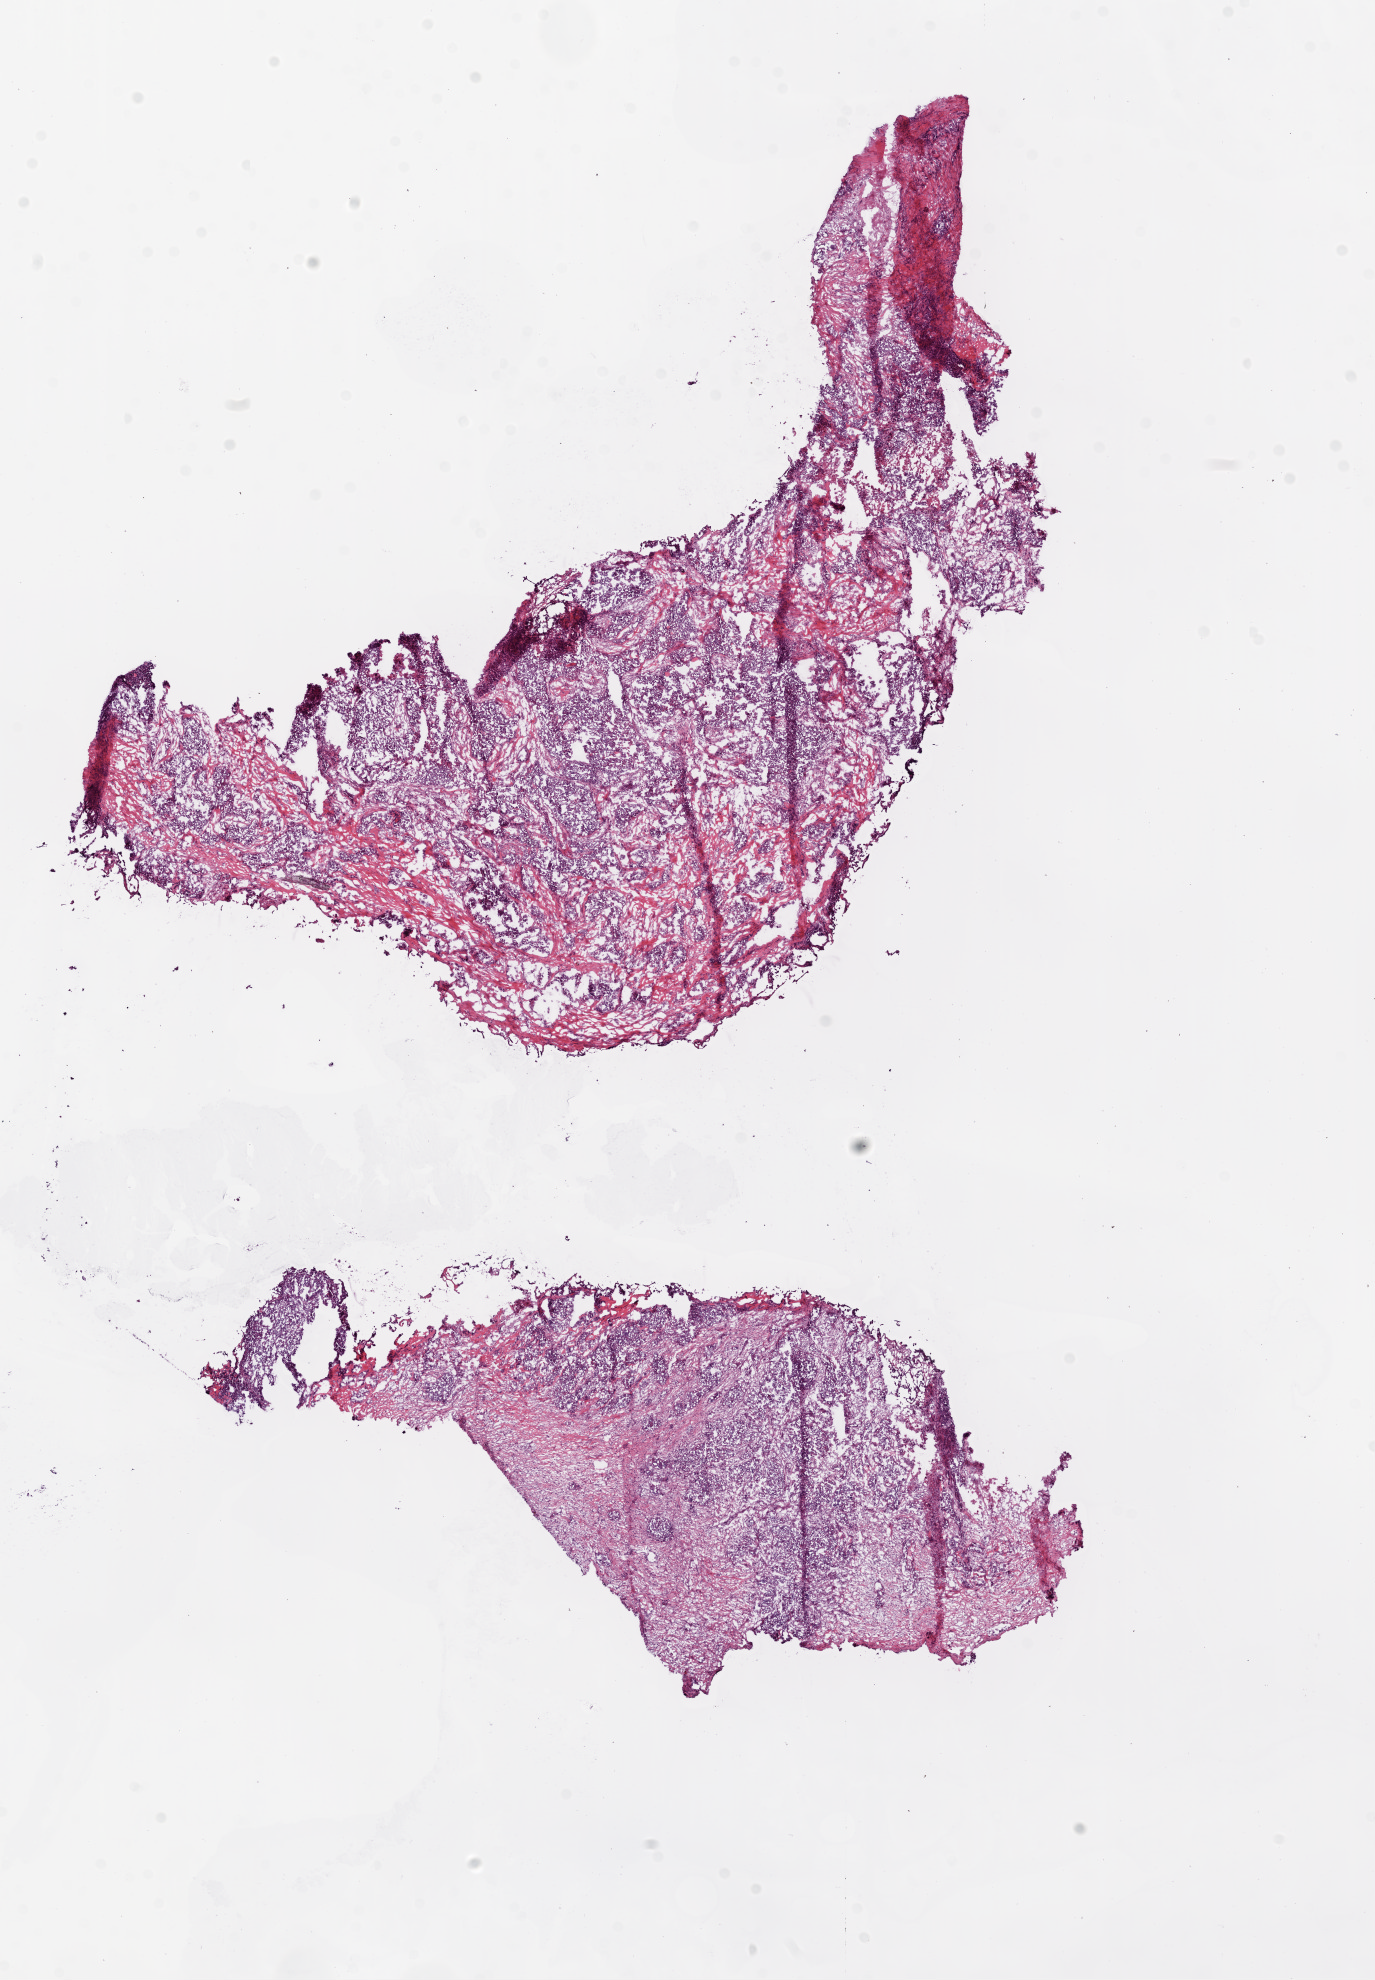
Digitized Hematoxylin and eosin (H&E) stained tissue section (whole slide), shown as a low-resolution overview of the whole scanned area (about 11.0 x 15.9 mm, acquisition: 20x scan); frozen section from the top of the tissue portion; primary tumour sample from the ovary. Female, age 55 years at initial diagnosis. Histologic grade: G3 (poorly differentiated). Pathologist review of this section (percent, as recorded): tumour cells 74%, tumour nuclei 89%, normal cells 25%, stromal cells 0%, necrosis 1%.
- laterality: bilateral
- FIGO stage: IIIC
- histologic diagnosis: Serous cystadenocarcinoma, NOS